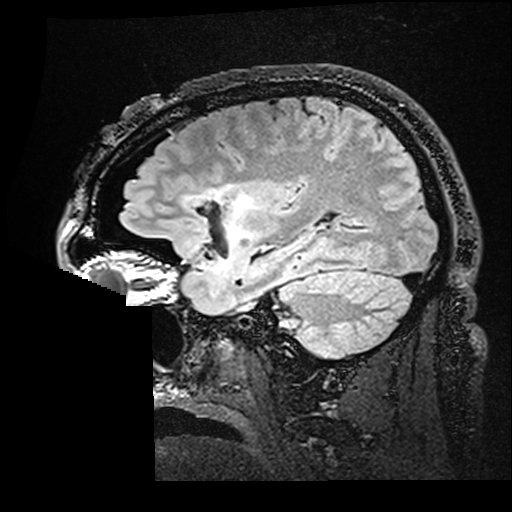
Brain MRI from a brain-tumour surgery series, one sagittal slice. Slice 119 of 176 in the series (ordered by position). T2 FLAIR. 512 × 512 image matrix, field of view 250 × 250 mm. From the clinical record (not read from this slice): histopathology: Astrocytoma; WHO grade: 2; IDH mutation: yes; tumour location: Right Insular.
Annotated regions visible in this slice (expert manual segmentation):
- residual tumour: bounding box [x1, y1, x2, y2] px = [182, 185, 259, 241]